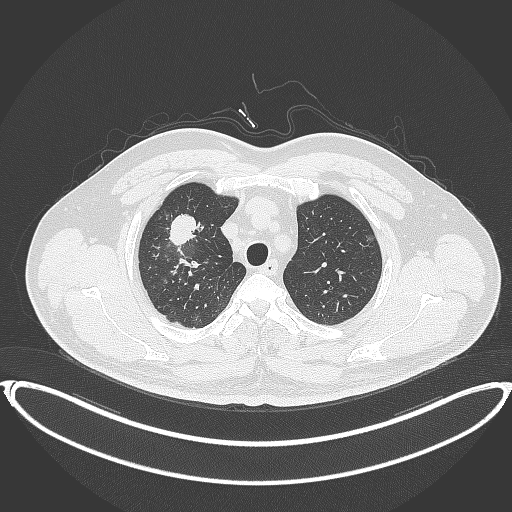
Chest CT, one axial slice. Position 313 of 399 along the scan axis. 120 kVp. Lung window (W 1500 / L -600 HU). 1 mm slice thickness. 512 × 512 image matrix, field of view 445 × 445 mm. Male patient, age 53 years. From the clinical record (not read from this slice): clinical TNM (as recorded): T2a N0 M0.
Structures marked on this image (rectangle marked by the reading radiologist):
- lung tumour (recorded histology: adenocarcinoma): box from (x=165, y=212) to (x=202, y=250) px